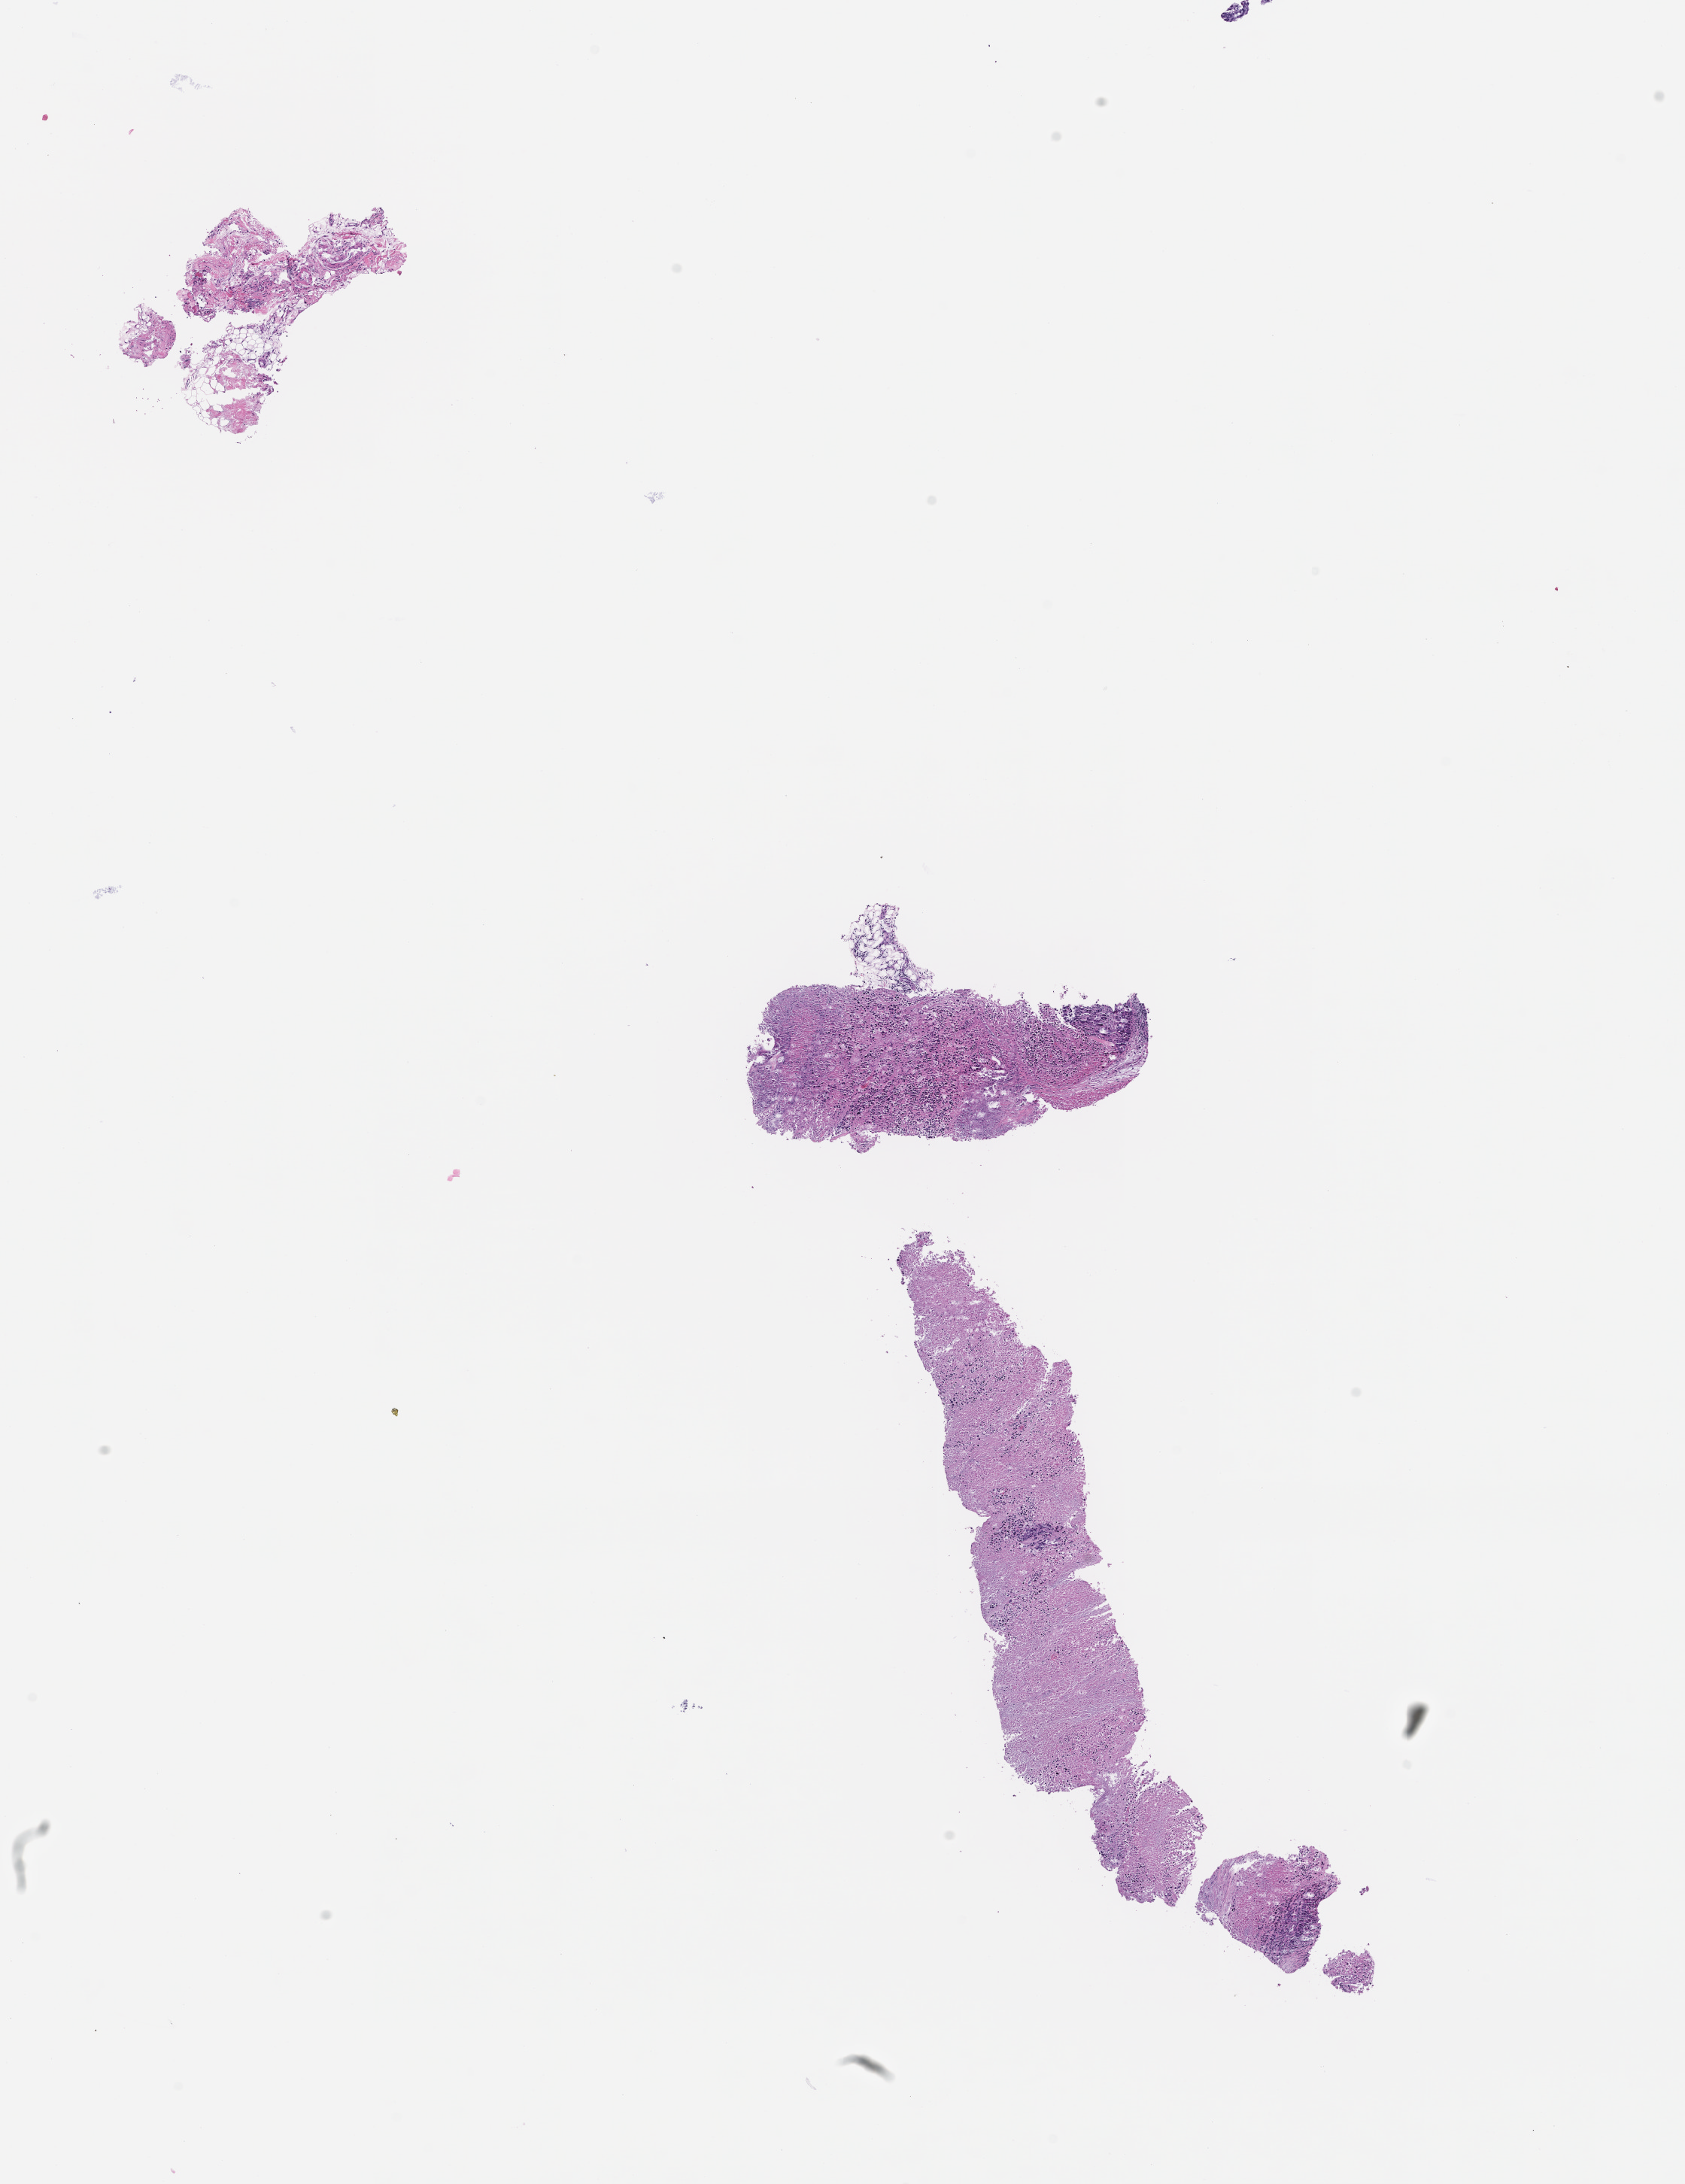
Haematoxylin and eosin whole-slide image — whole scanned area (about 9.0 x 11.7 mm) shown as a low-resolution overview; formalin-fixed paraffin-embedded section. Patient: female.
This section: metastasis (sampled organ not recorded). Primary diagnosis of the patient: Colorectal Carcinoma.